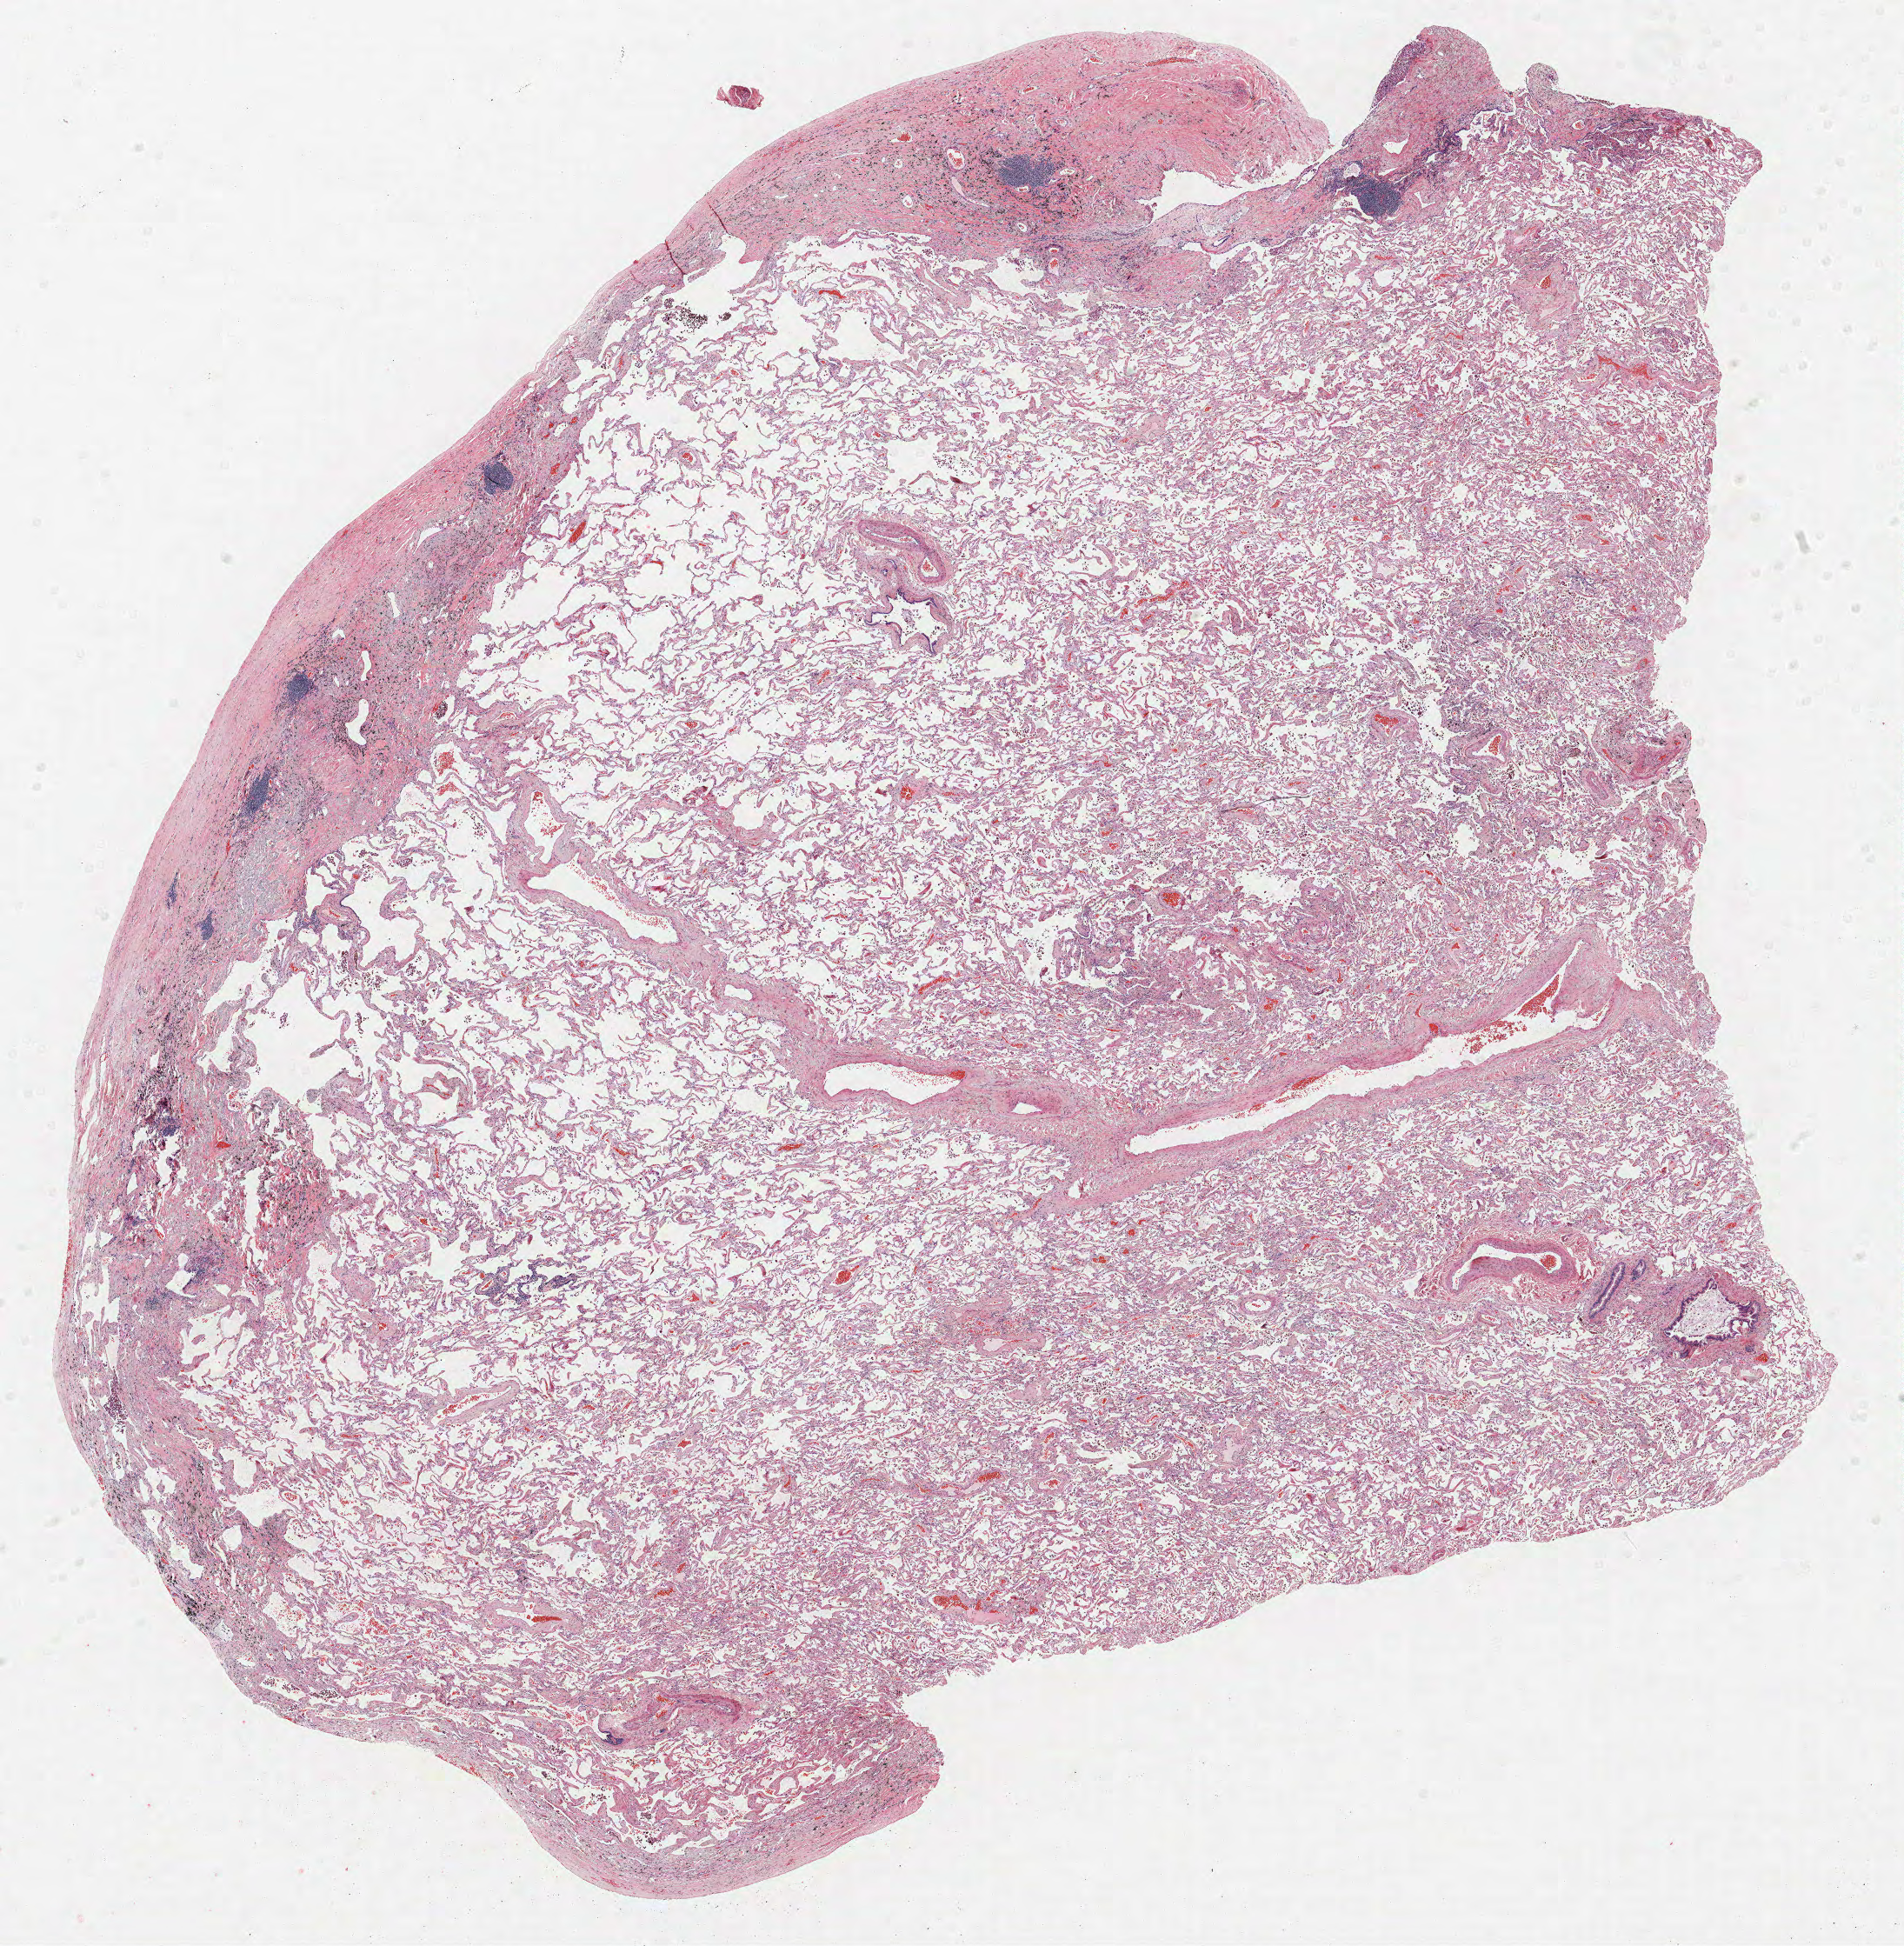
Hematoxylin and eosin (H&E) stained whole-slide image, shown as a low-resolution overview of the whole scanned area (about 17.5 x 17.9 mm, from a 40x scan); formalin-fixed paraffin-embedded (FFPE) section; lung tissue. Male patient, aged 69 at enrolment.
Participant's lung-cancer diagnosis: Adenocarcinoma, NOS.